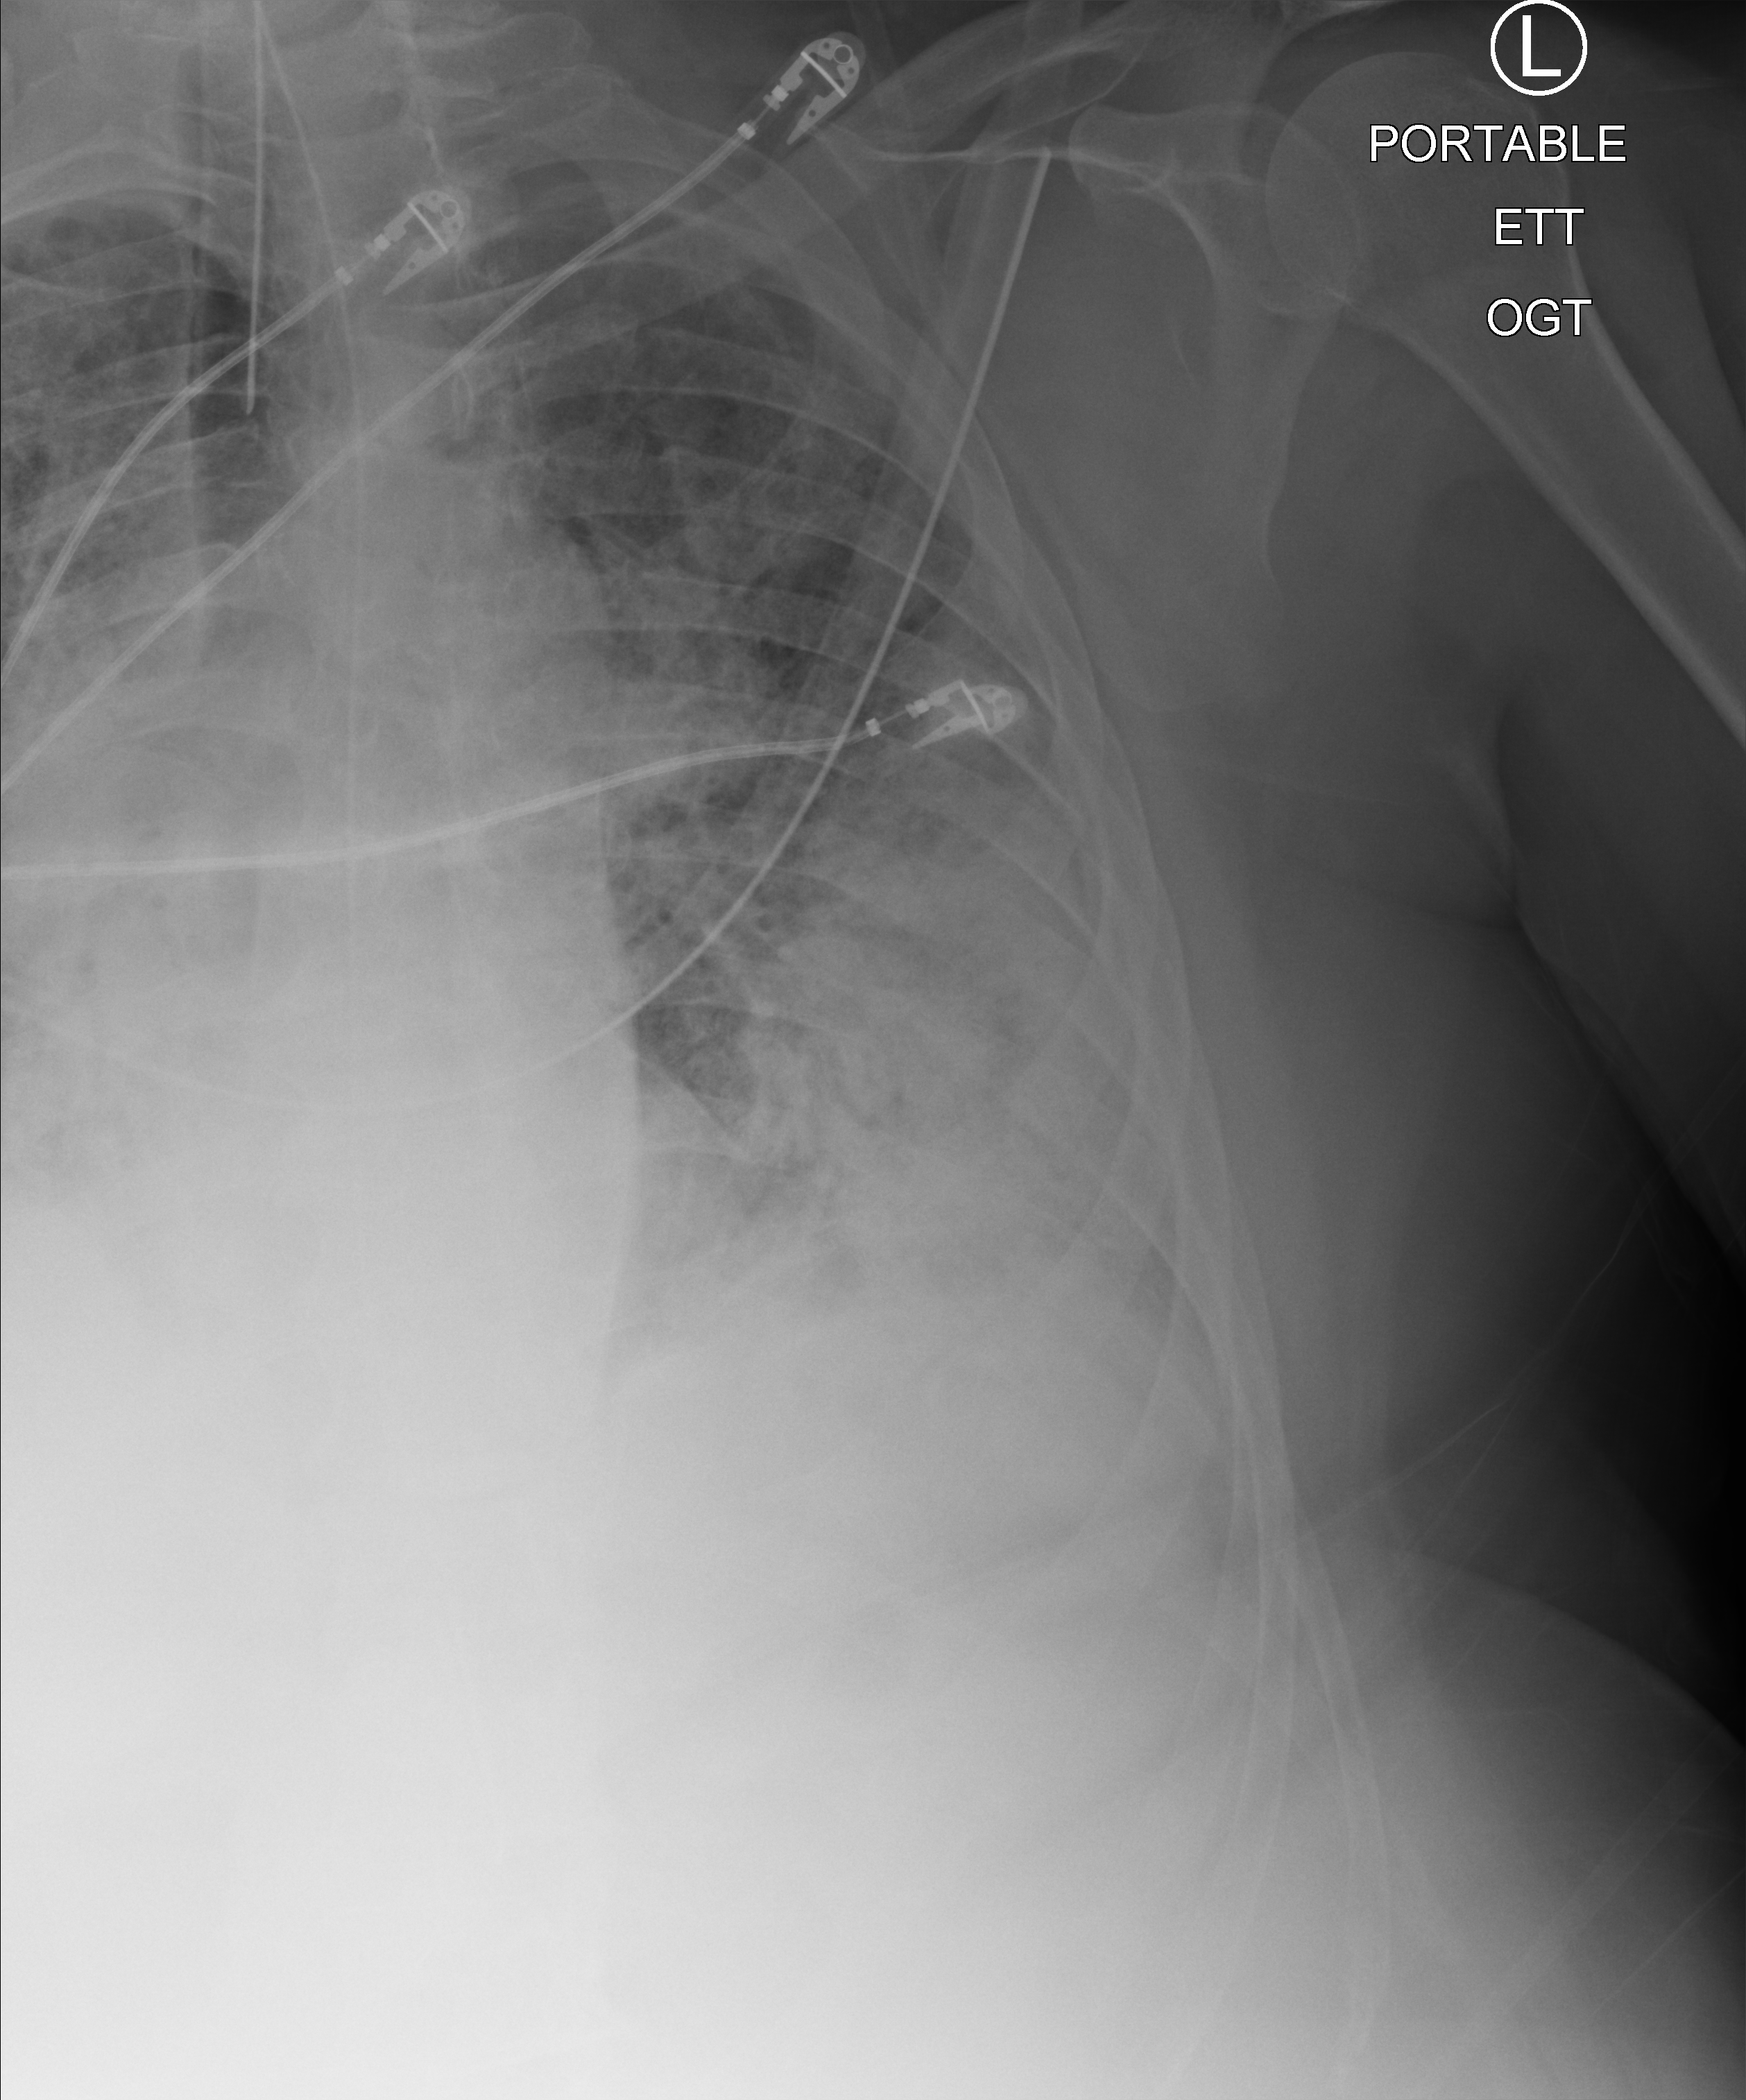
Chest X-ray (portable); anteroposterior (AP) projection. Patient hospitalised with COVID-19; male, aged 60–74 years.
Admission-level facts for this patient (not findings on this image; timing relative to this image not recorded): mechanically ventilated during this hospital stay: yes.